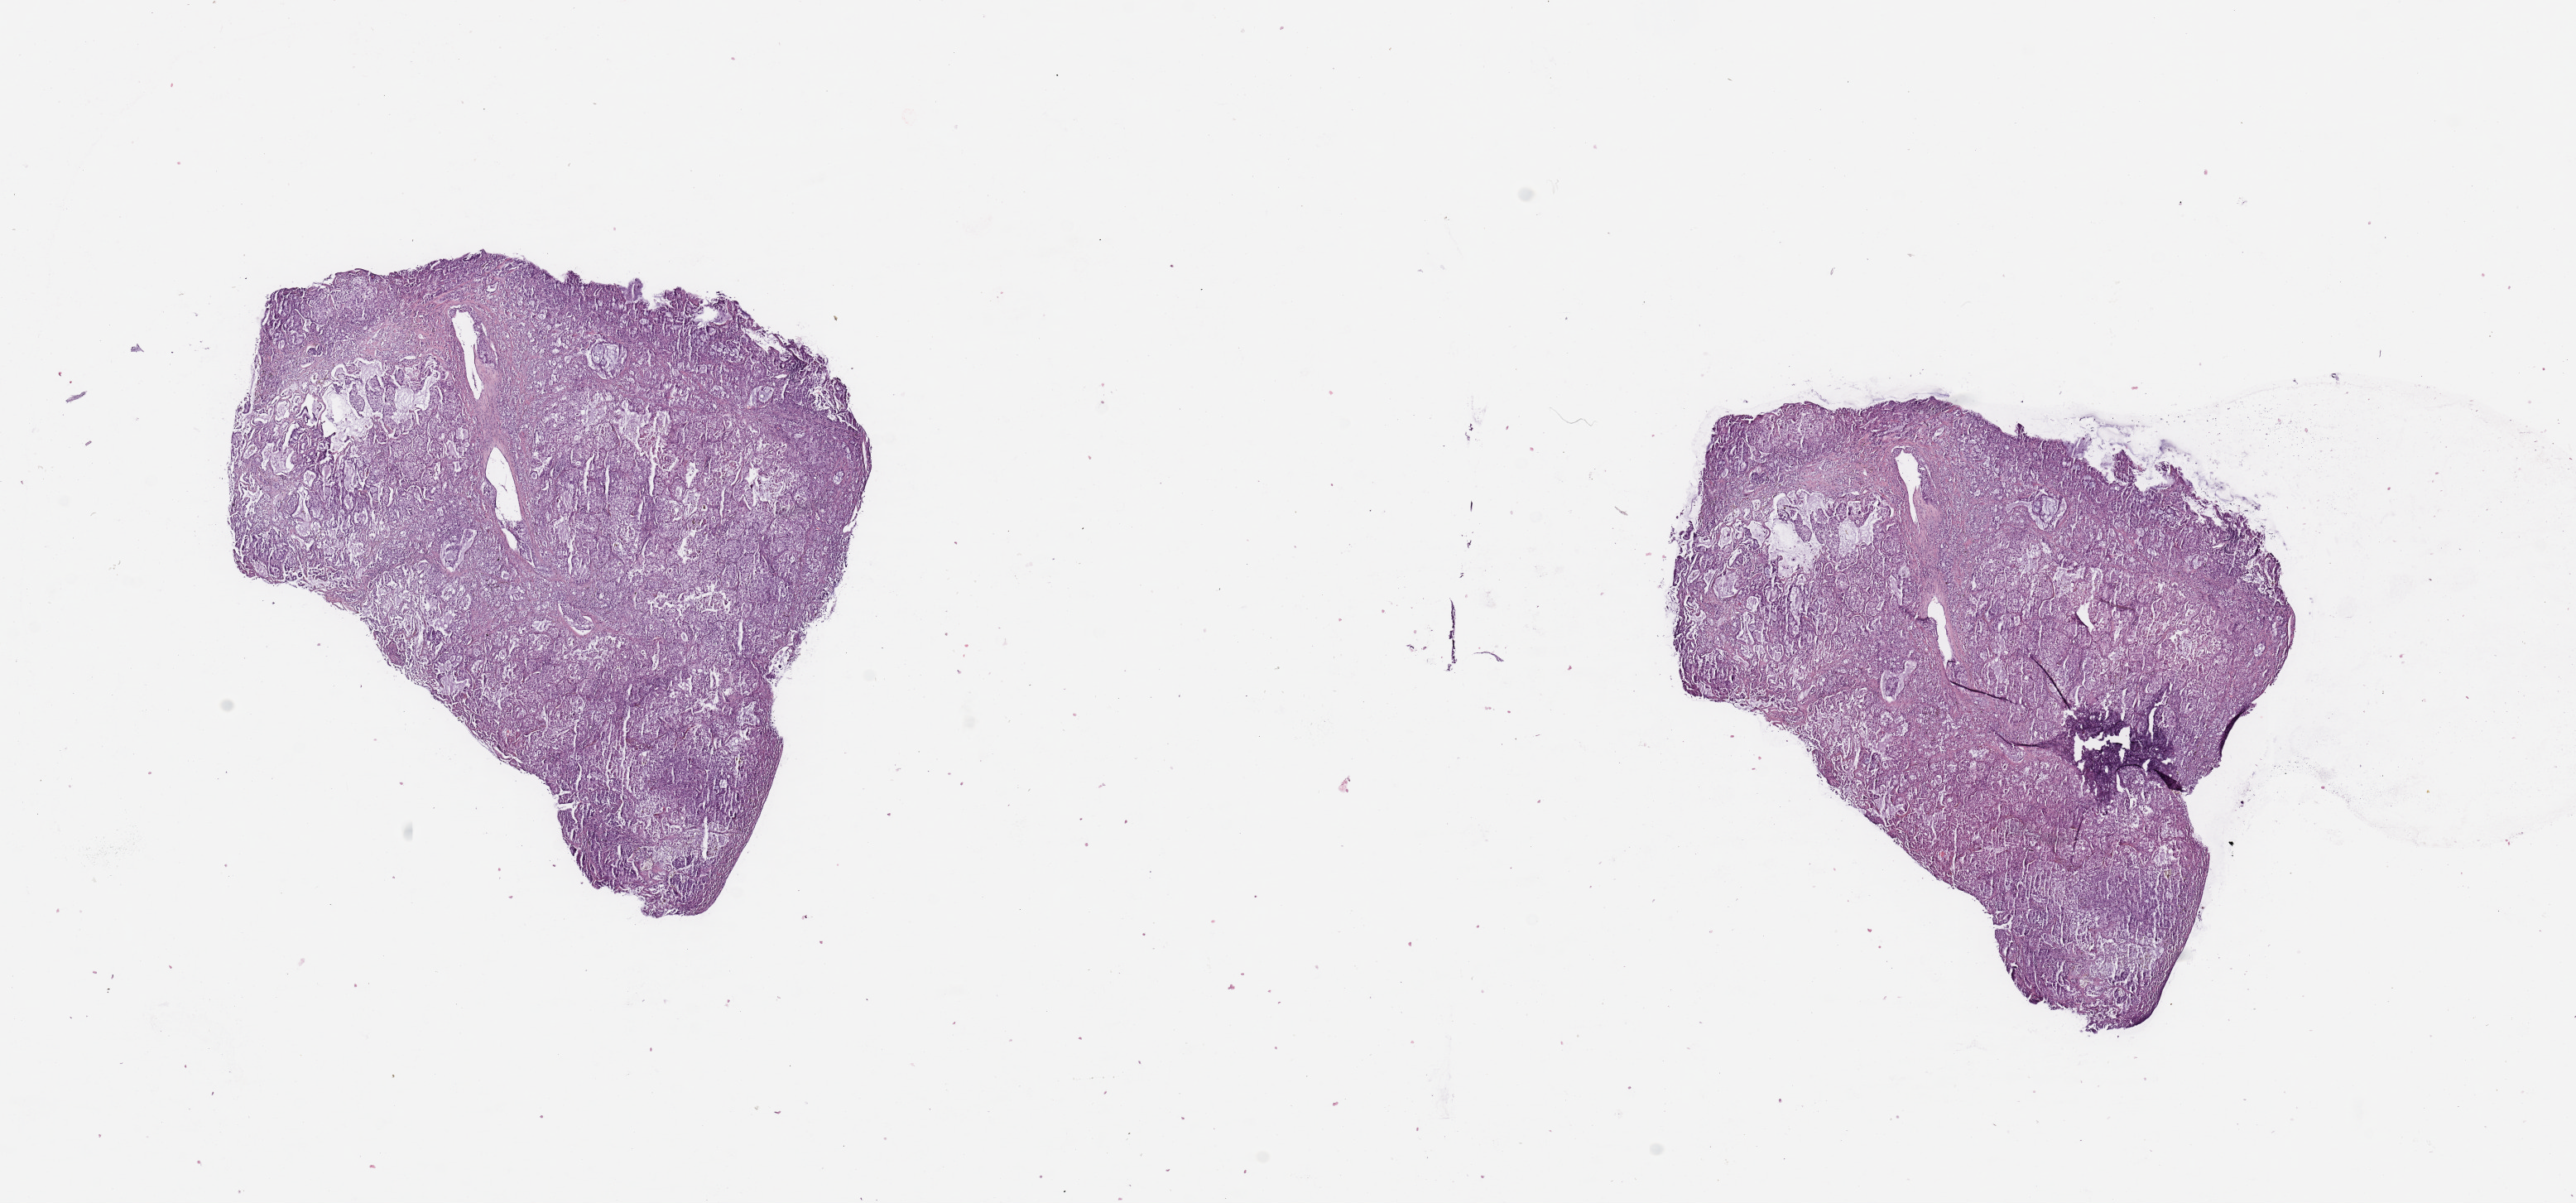
Whole-slide histology image, H&E-stained, low-resolution overview of the scanned area, about 24.6 x 11.5 mm (from a 20x scan). Tumour tissue sample, lung. Patient: male, age 51 years. Histologic grade: G2 (moderately differentiated).
Histologic diagnosis: Adenocarcinoma, NOS. AJCC pathologic stage: IIIA.